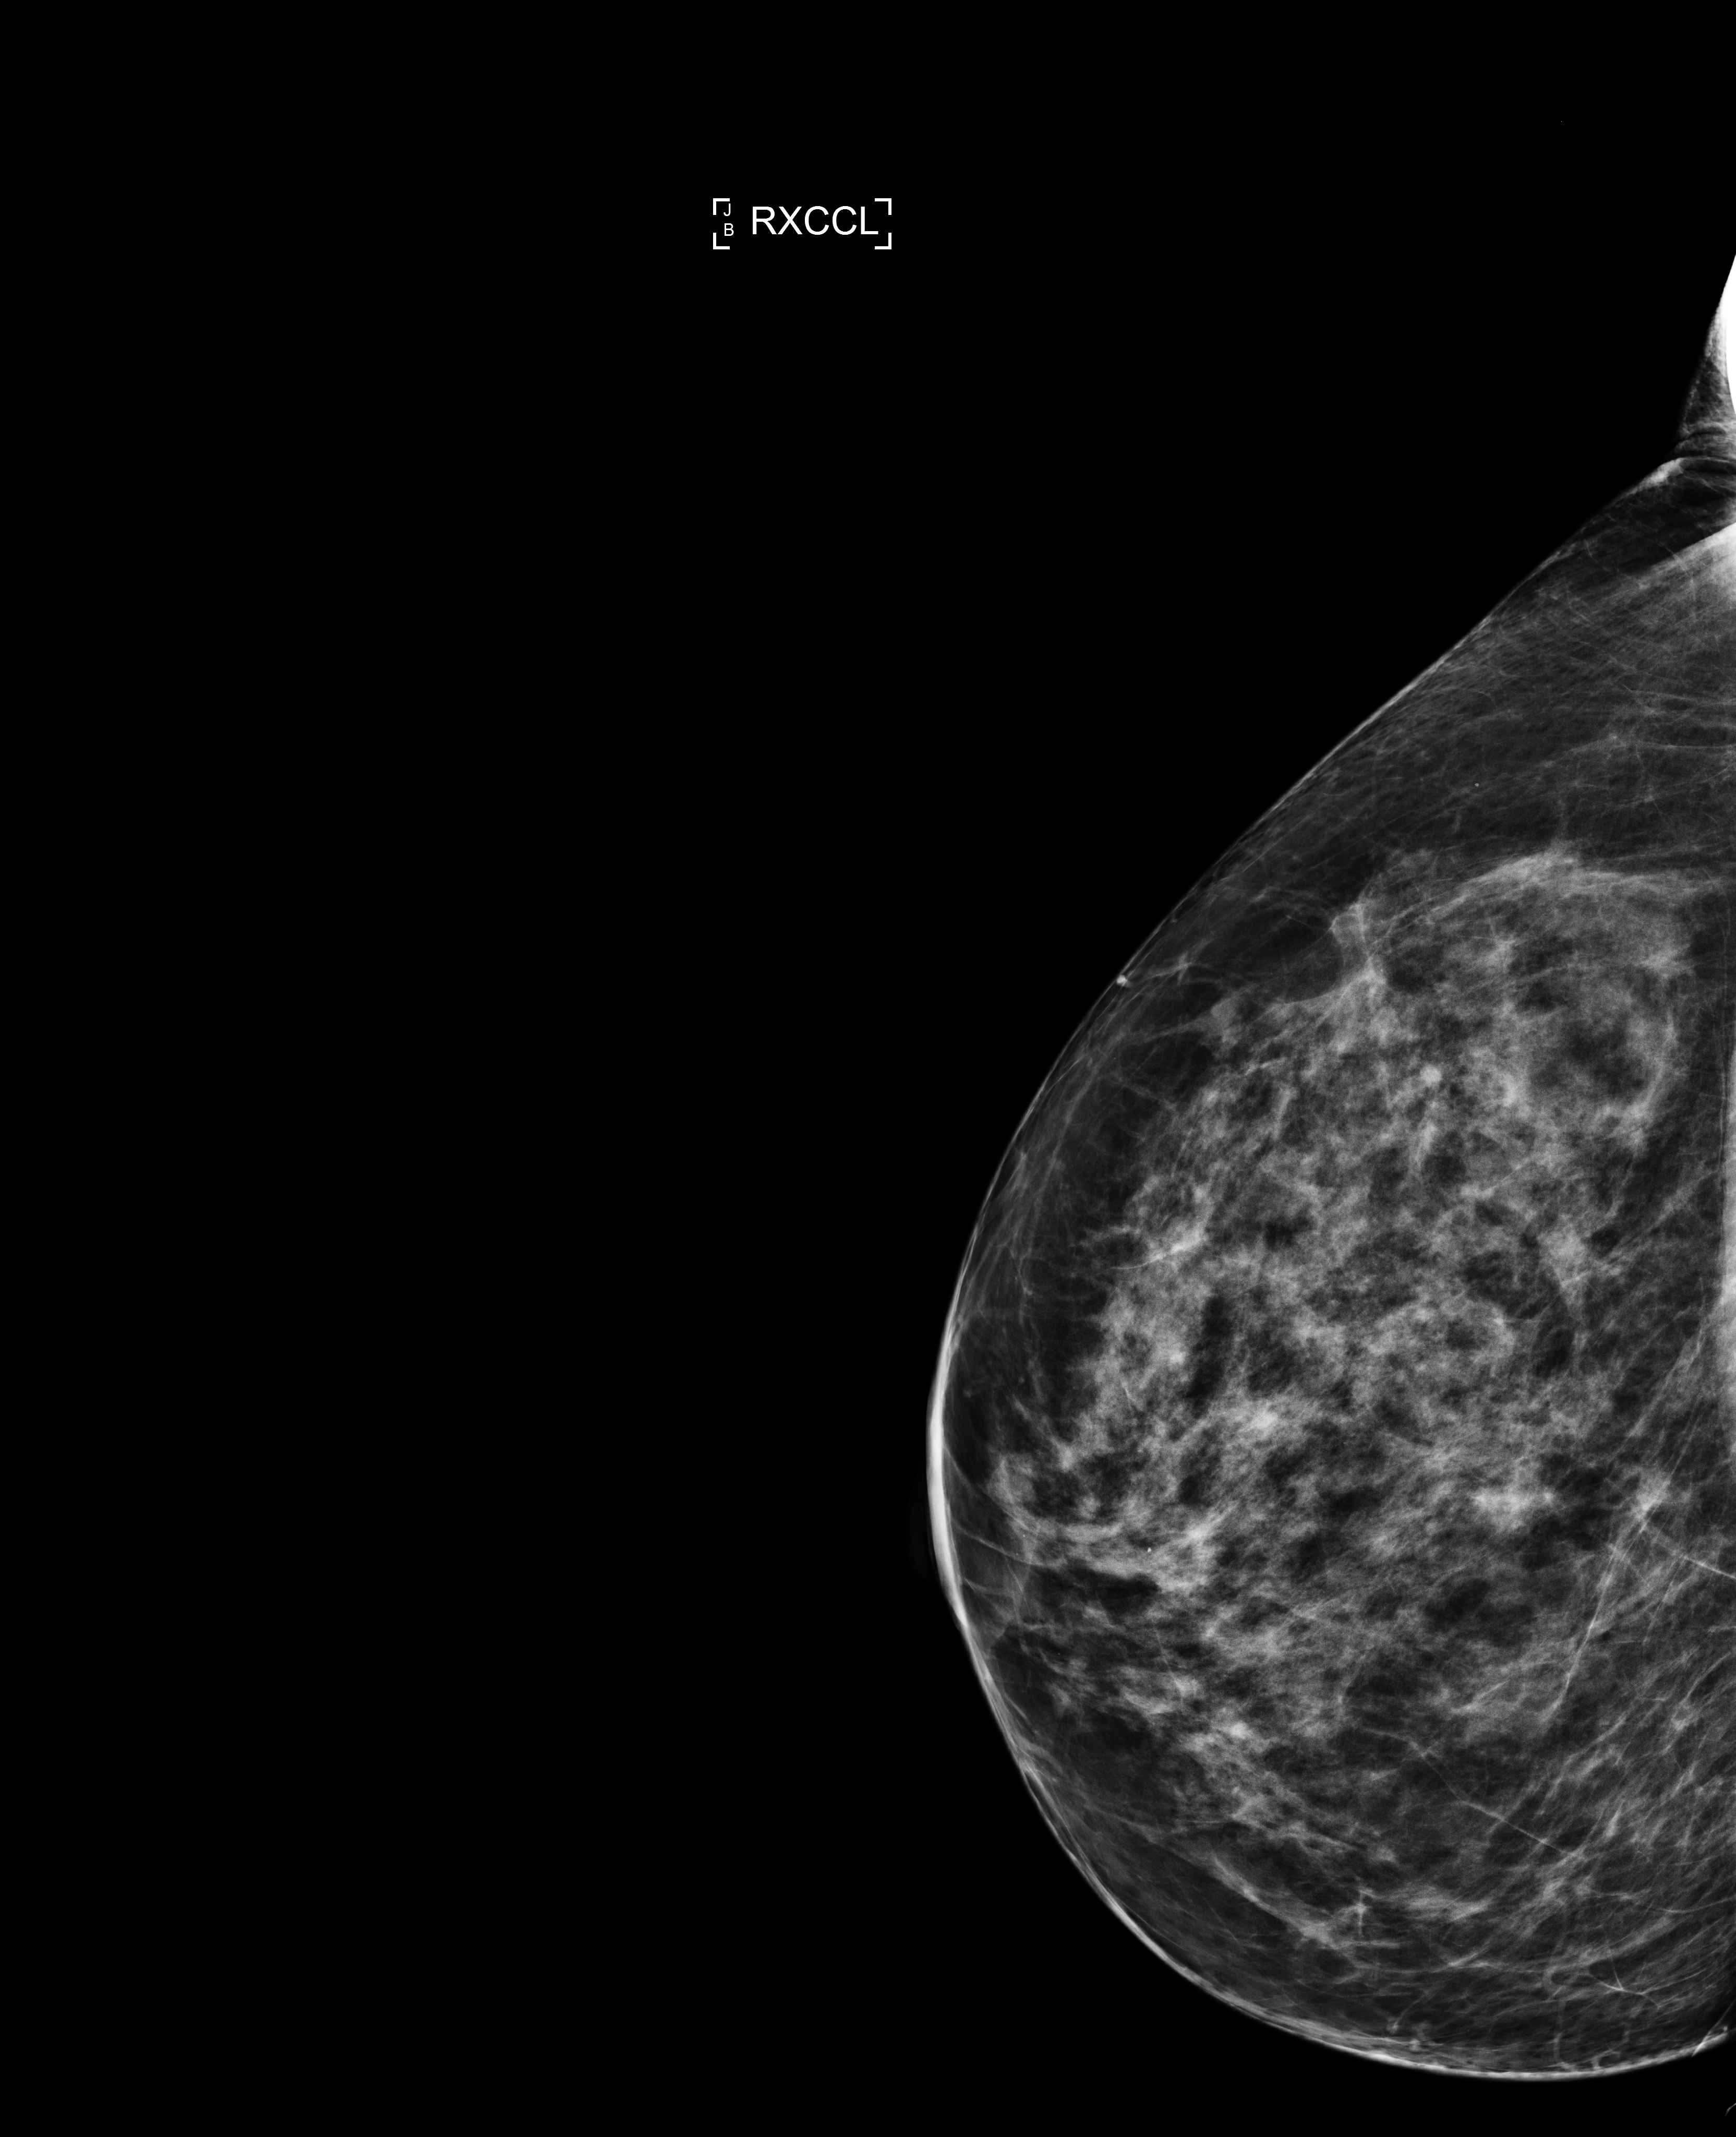
Screening examination, compressed breast thickness 85 mm. Patient aged 47 years (female).
Image type: full-field digital mammogram. Breast: right. Projection: laterally exaggerated craniocaudal (XCCL) view. Breast density at the screening exam (both breasts): heterogeneously dense (BI-RADS density category c). Final BI-RADS category for the screening round (tomosynthesis exam, both breasts): category 1. Recall: no recall after this screen.